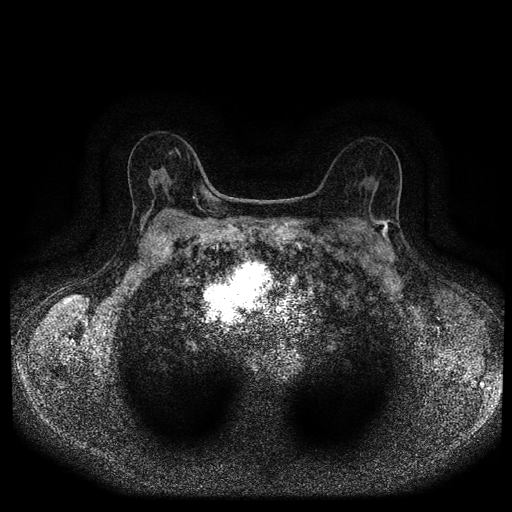
Breast MRI (dynamic contrast-enhanced, multi-phase), one axial slice. Position 62 of 116 along the scan axis. Dynamic contrast-enhanced series, time point 2 of 5 at this slice position (early post-contrast). 1.5 T. TE 2.7 ms, TR 5.4 ms. 2 mm slice thickness. 512 × 512 image matrix, field of view 330 × 330 mm. Female patient, age 63 years.
Structures marked on this image (semi-automatically segmented with operator editing):
- breast lesion (labelled 'tumour' in the annotation; benign lesions carry a separate 'benign' label): bounding box (x1, y1, x2, y2) in pixels: (371, 216, 394, 239)